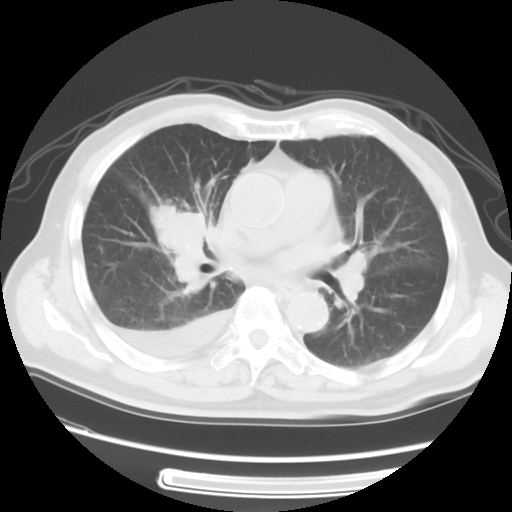
Chest CT, one axial slice; position 29 of 56 along the scan axis; reconstruction kernel STANDARD; 120 kVp; lung window (W 1500 / L -600 HU); 5 mm slice thickness; 512 × 512 image matrix, field of view 360 × 360 mm. Male patient, age 77 years. Case-level facts recorded for this patient, not image findings: clinical TNM (as recorded): T3 N3 M1b; histopathological grade: G3.
Structures marked on this image (bounding box drawn by a radiologist):
- lung tumour (recorded histology: small cell carcinoma): box from (x=139, y=191) to (x=215, y=296) px